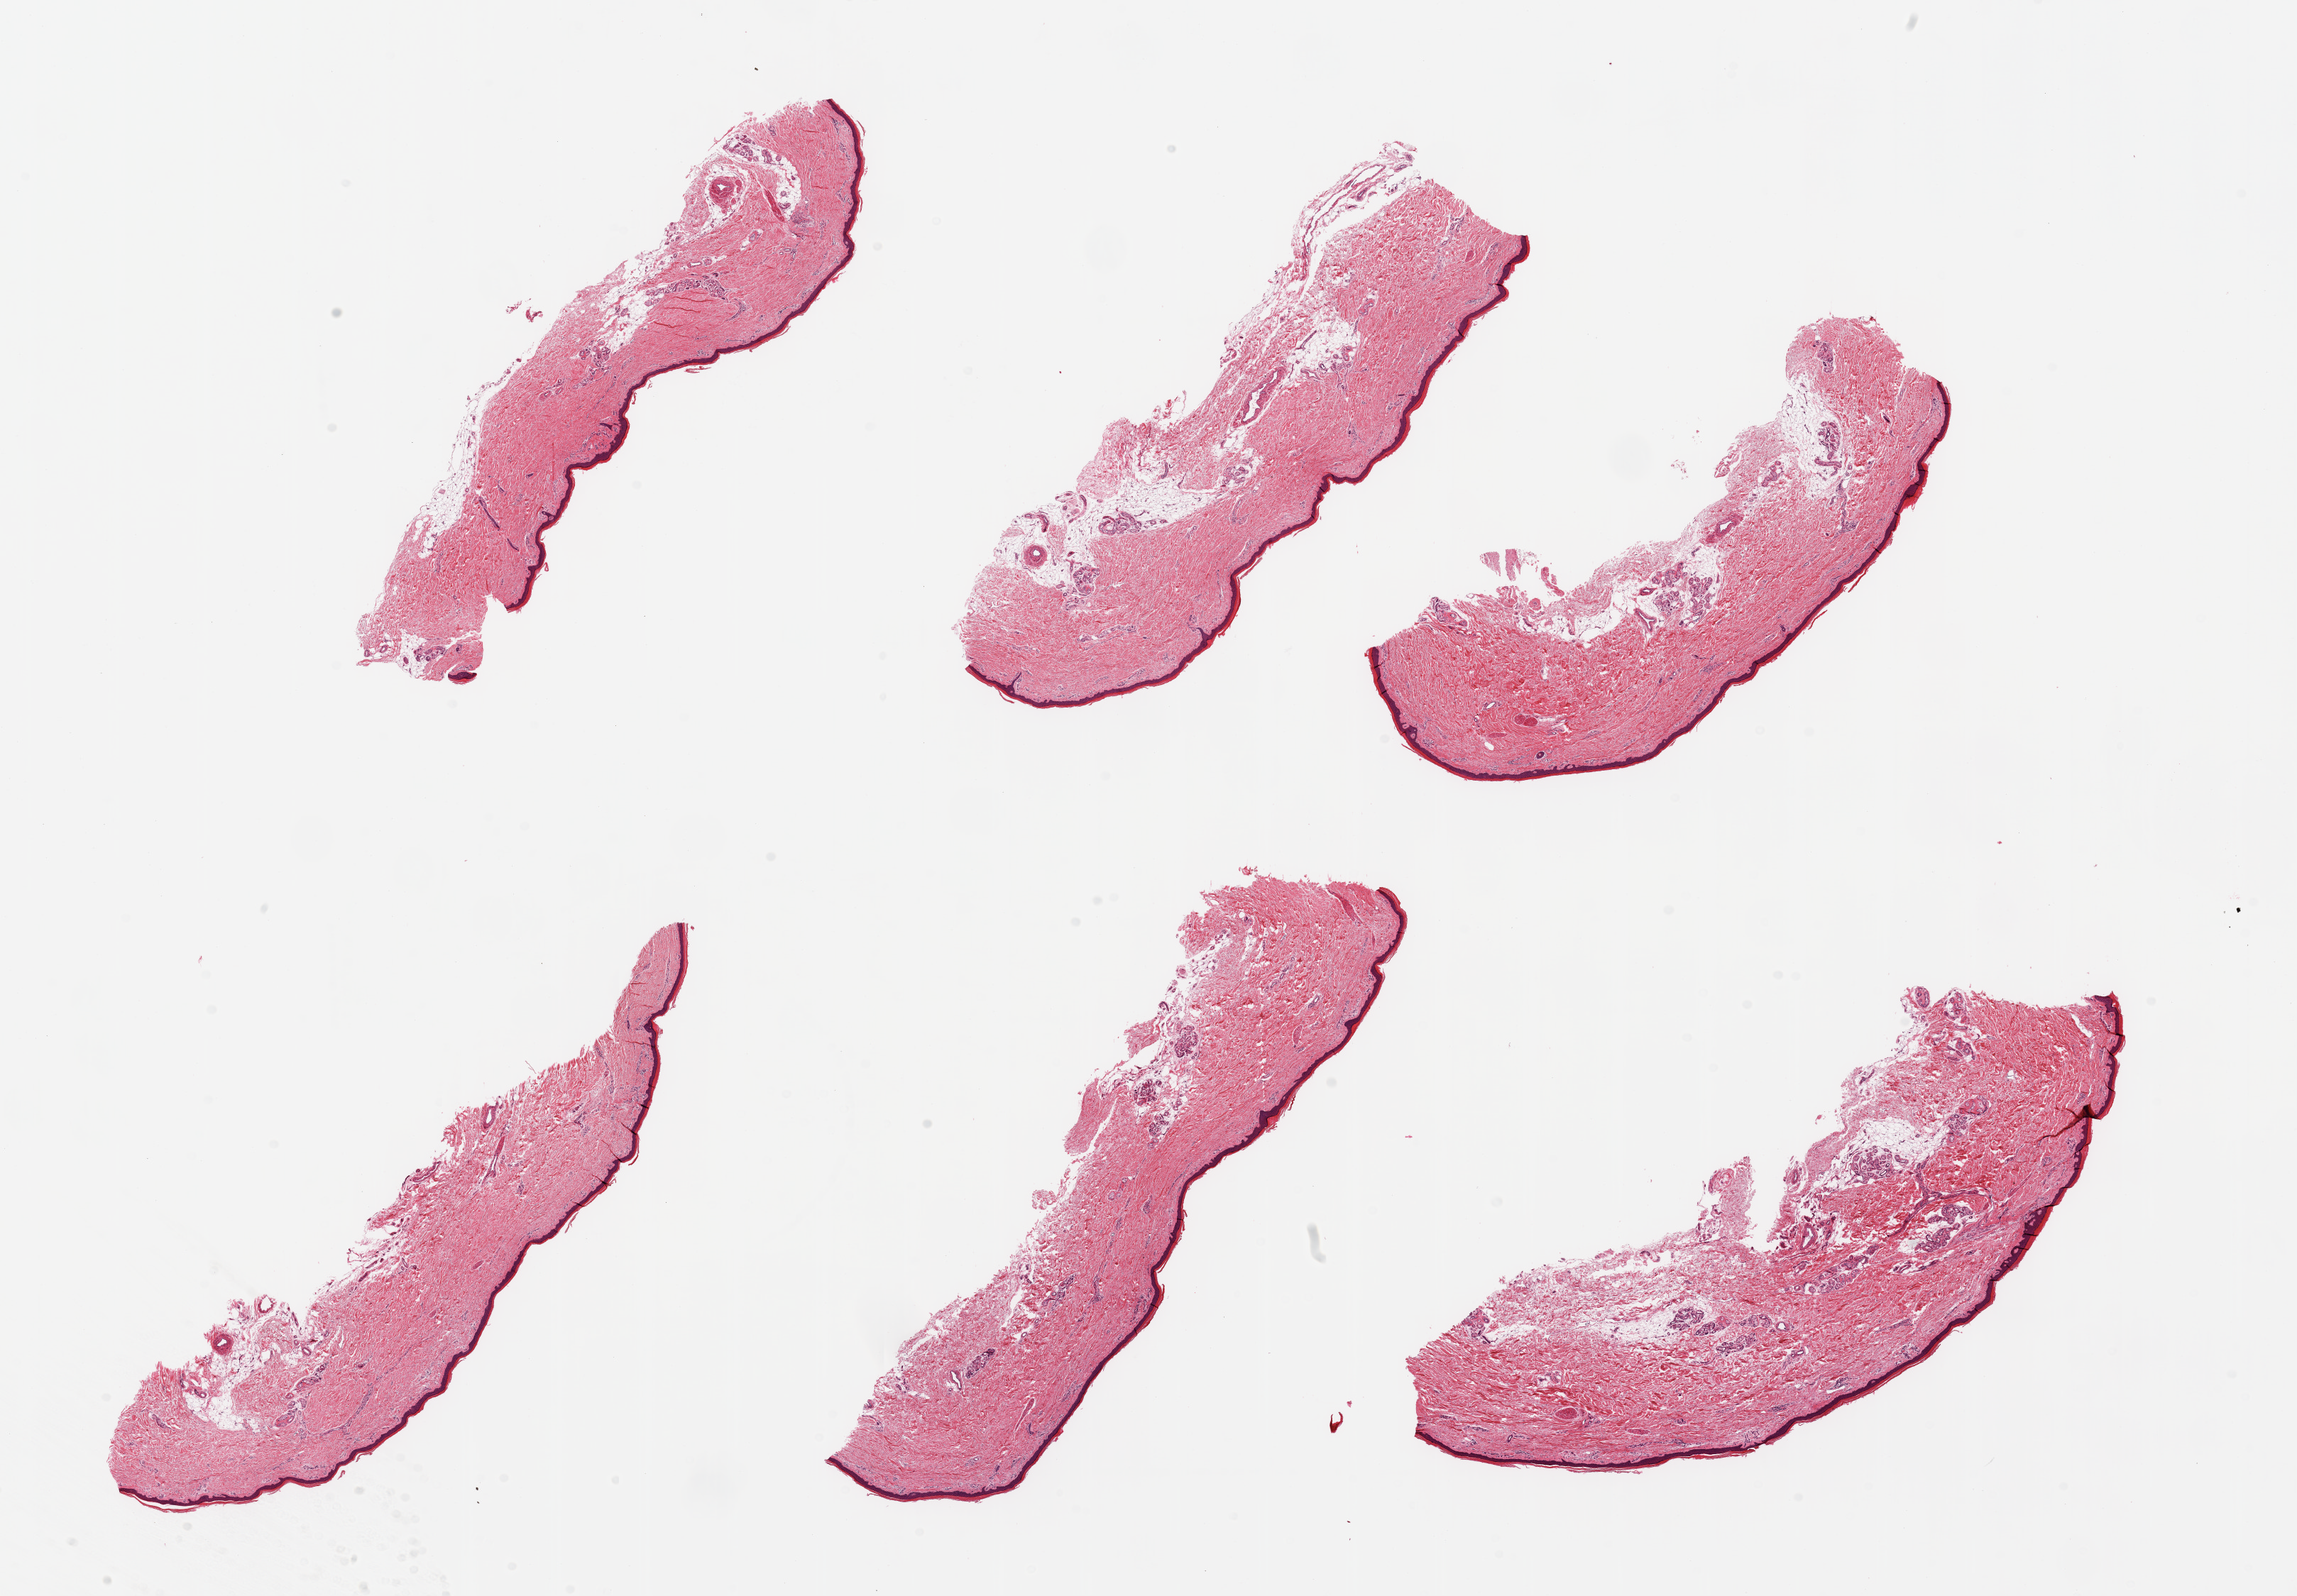
Haematoxylin and eosin whole-slide image — low-resolution overview of the scanned area, about 25.6 x 17.8 mm; PAXgene-fixed paraffin-embedded (PFPE) section; target tissue: skin of lower leg; tissue donor sample. Donor: male.
Reviewer comment on this tissue sample: 6 pieces; well trimmed; 5-10% dermal fat.